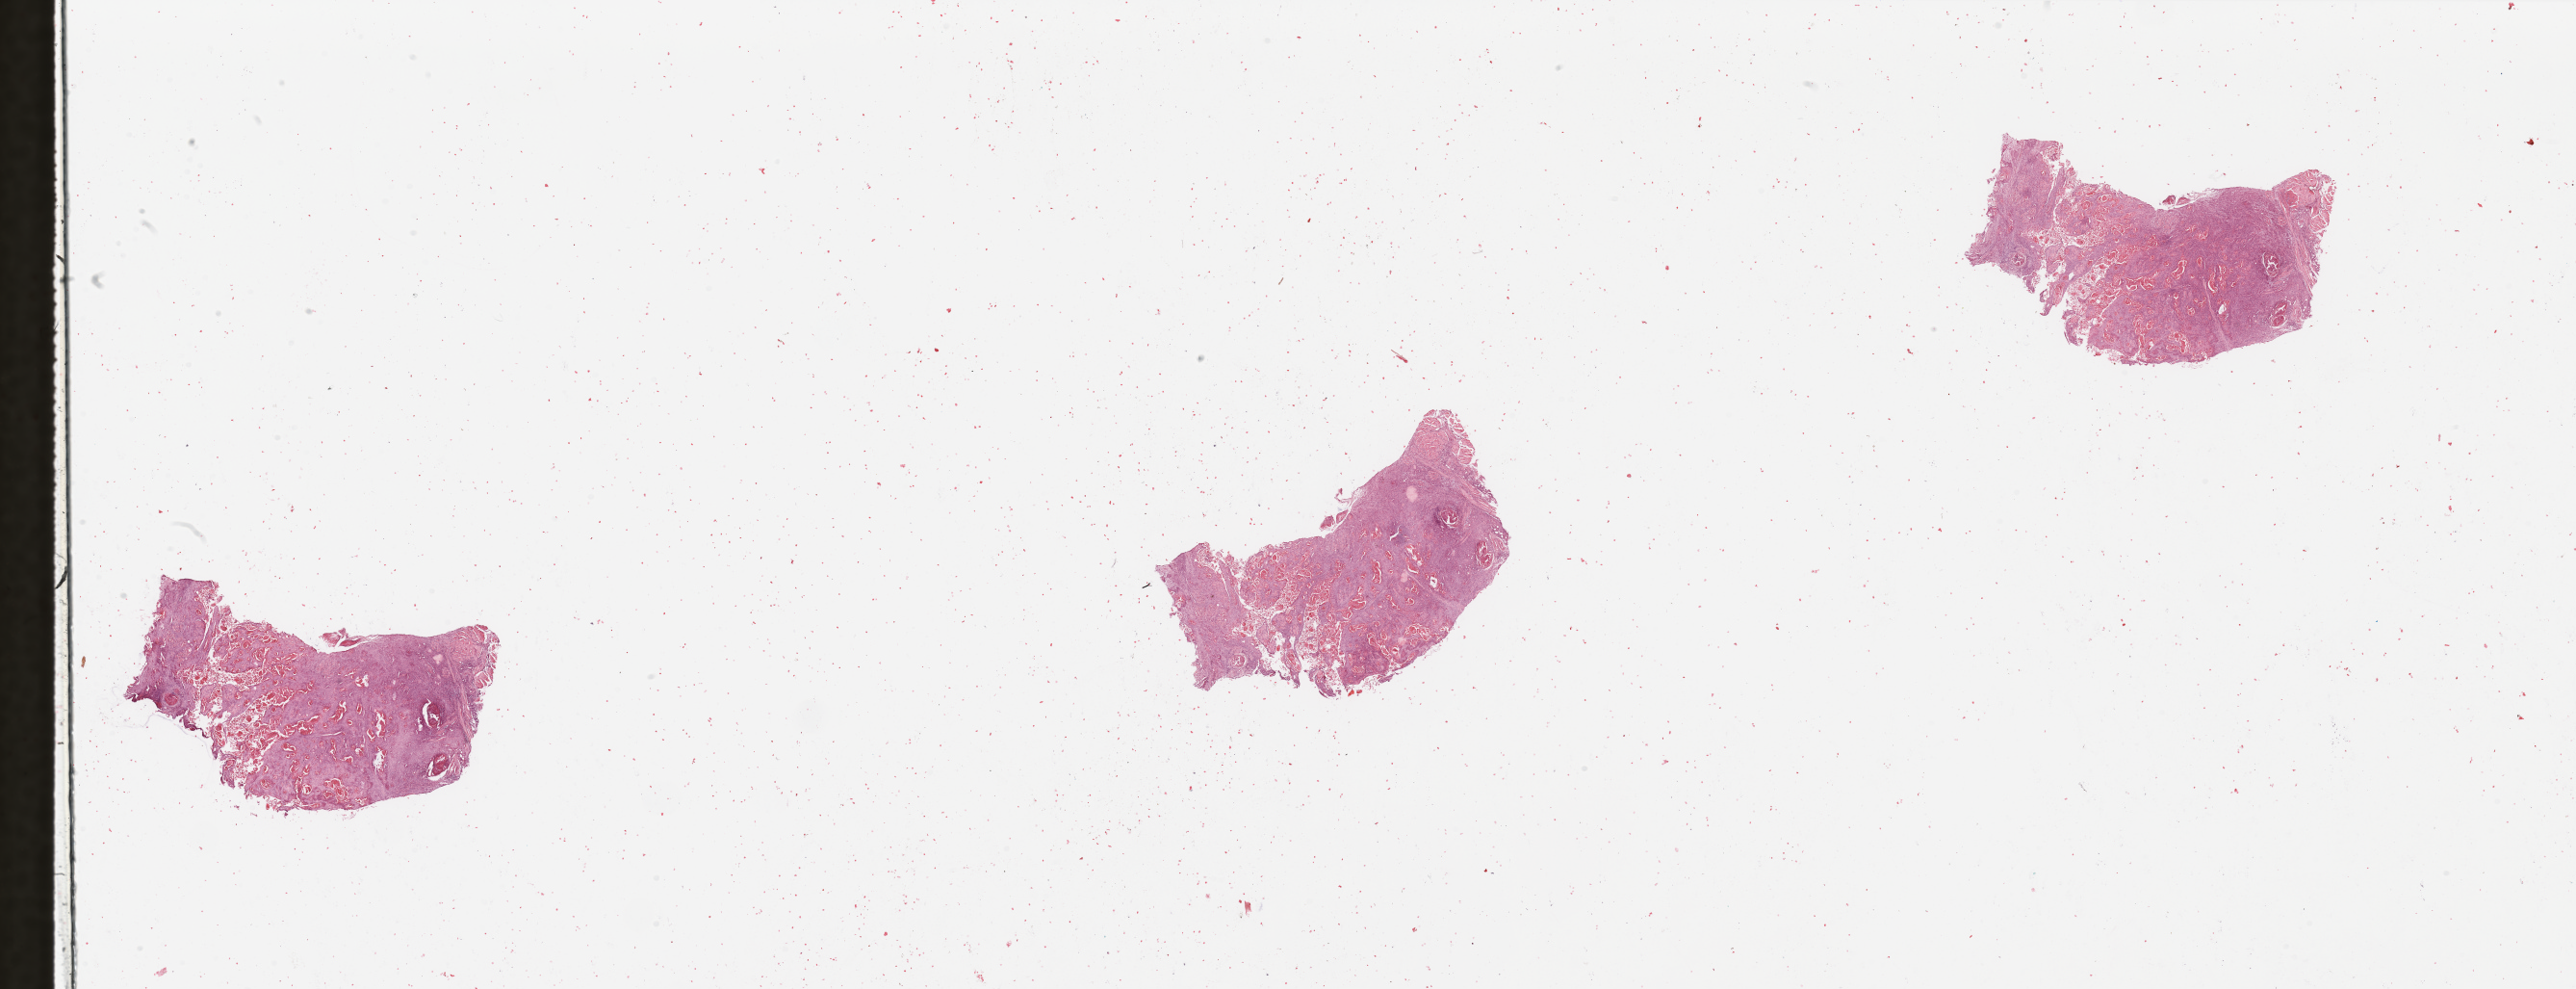
Whole-slide histology image, Hematoxylin and eosin (H&E) stained, a low-resolution overview of the entire scanned area, about 42.3 x 16.2 mm (slide scanned at 20x), tumour tissue sample, sampled site: floor of mouth. Patient: male, age 59 years. Histologic grade: G2 (moderately differentiated). Pathologist review of this section (percent, as recorded): tumour nuclei 80%, necrosis 7%.
Histologic diagnosis: Squamous cell carcinoma, NOS (floor of mouth, NOS). AJCC pathologic stage: IVA. Primary tumour site (as recorded): oral cavity.